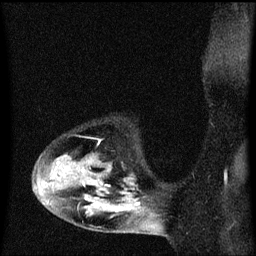
Breast MRI (dynamic contrast-enhanced), one sagittal slice; position 45 of 60 along the scan axis; dynamic contrast-enhanced series, image 2 of 3 at this slice position (ordered by acquisition); 1.5 T; TE 4.2 ms, TR 8.4 ms; 2 mm slice thickness; 256 × 256 image matrix. Female patient, age 49 years. From the clinical record (not read from this slice): setting: breast cancer imaged before/during neoadjuvant chemotherapy; receptor status: HR-positive, HER2-negative.
Structures marked on this image (semi-automatic segmentation, software-assisted and operator-edited):
- analysis volume of interest (the breast-tissue region the enhancement analysis was run in; not a lesion): bounding box [x1, y1, x2, y2] px = [34, 152, 160, 221]
- tumour enhancement mask (voxels above the 70 % enhancement threshold inside the analysis volume of interest): [83, 170, 139, 205]